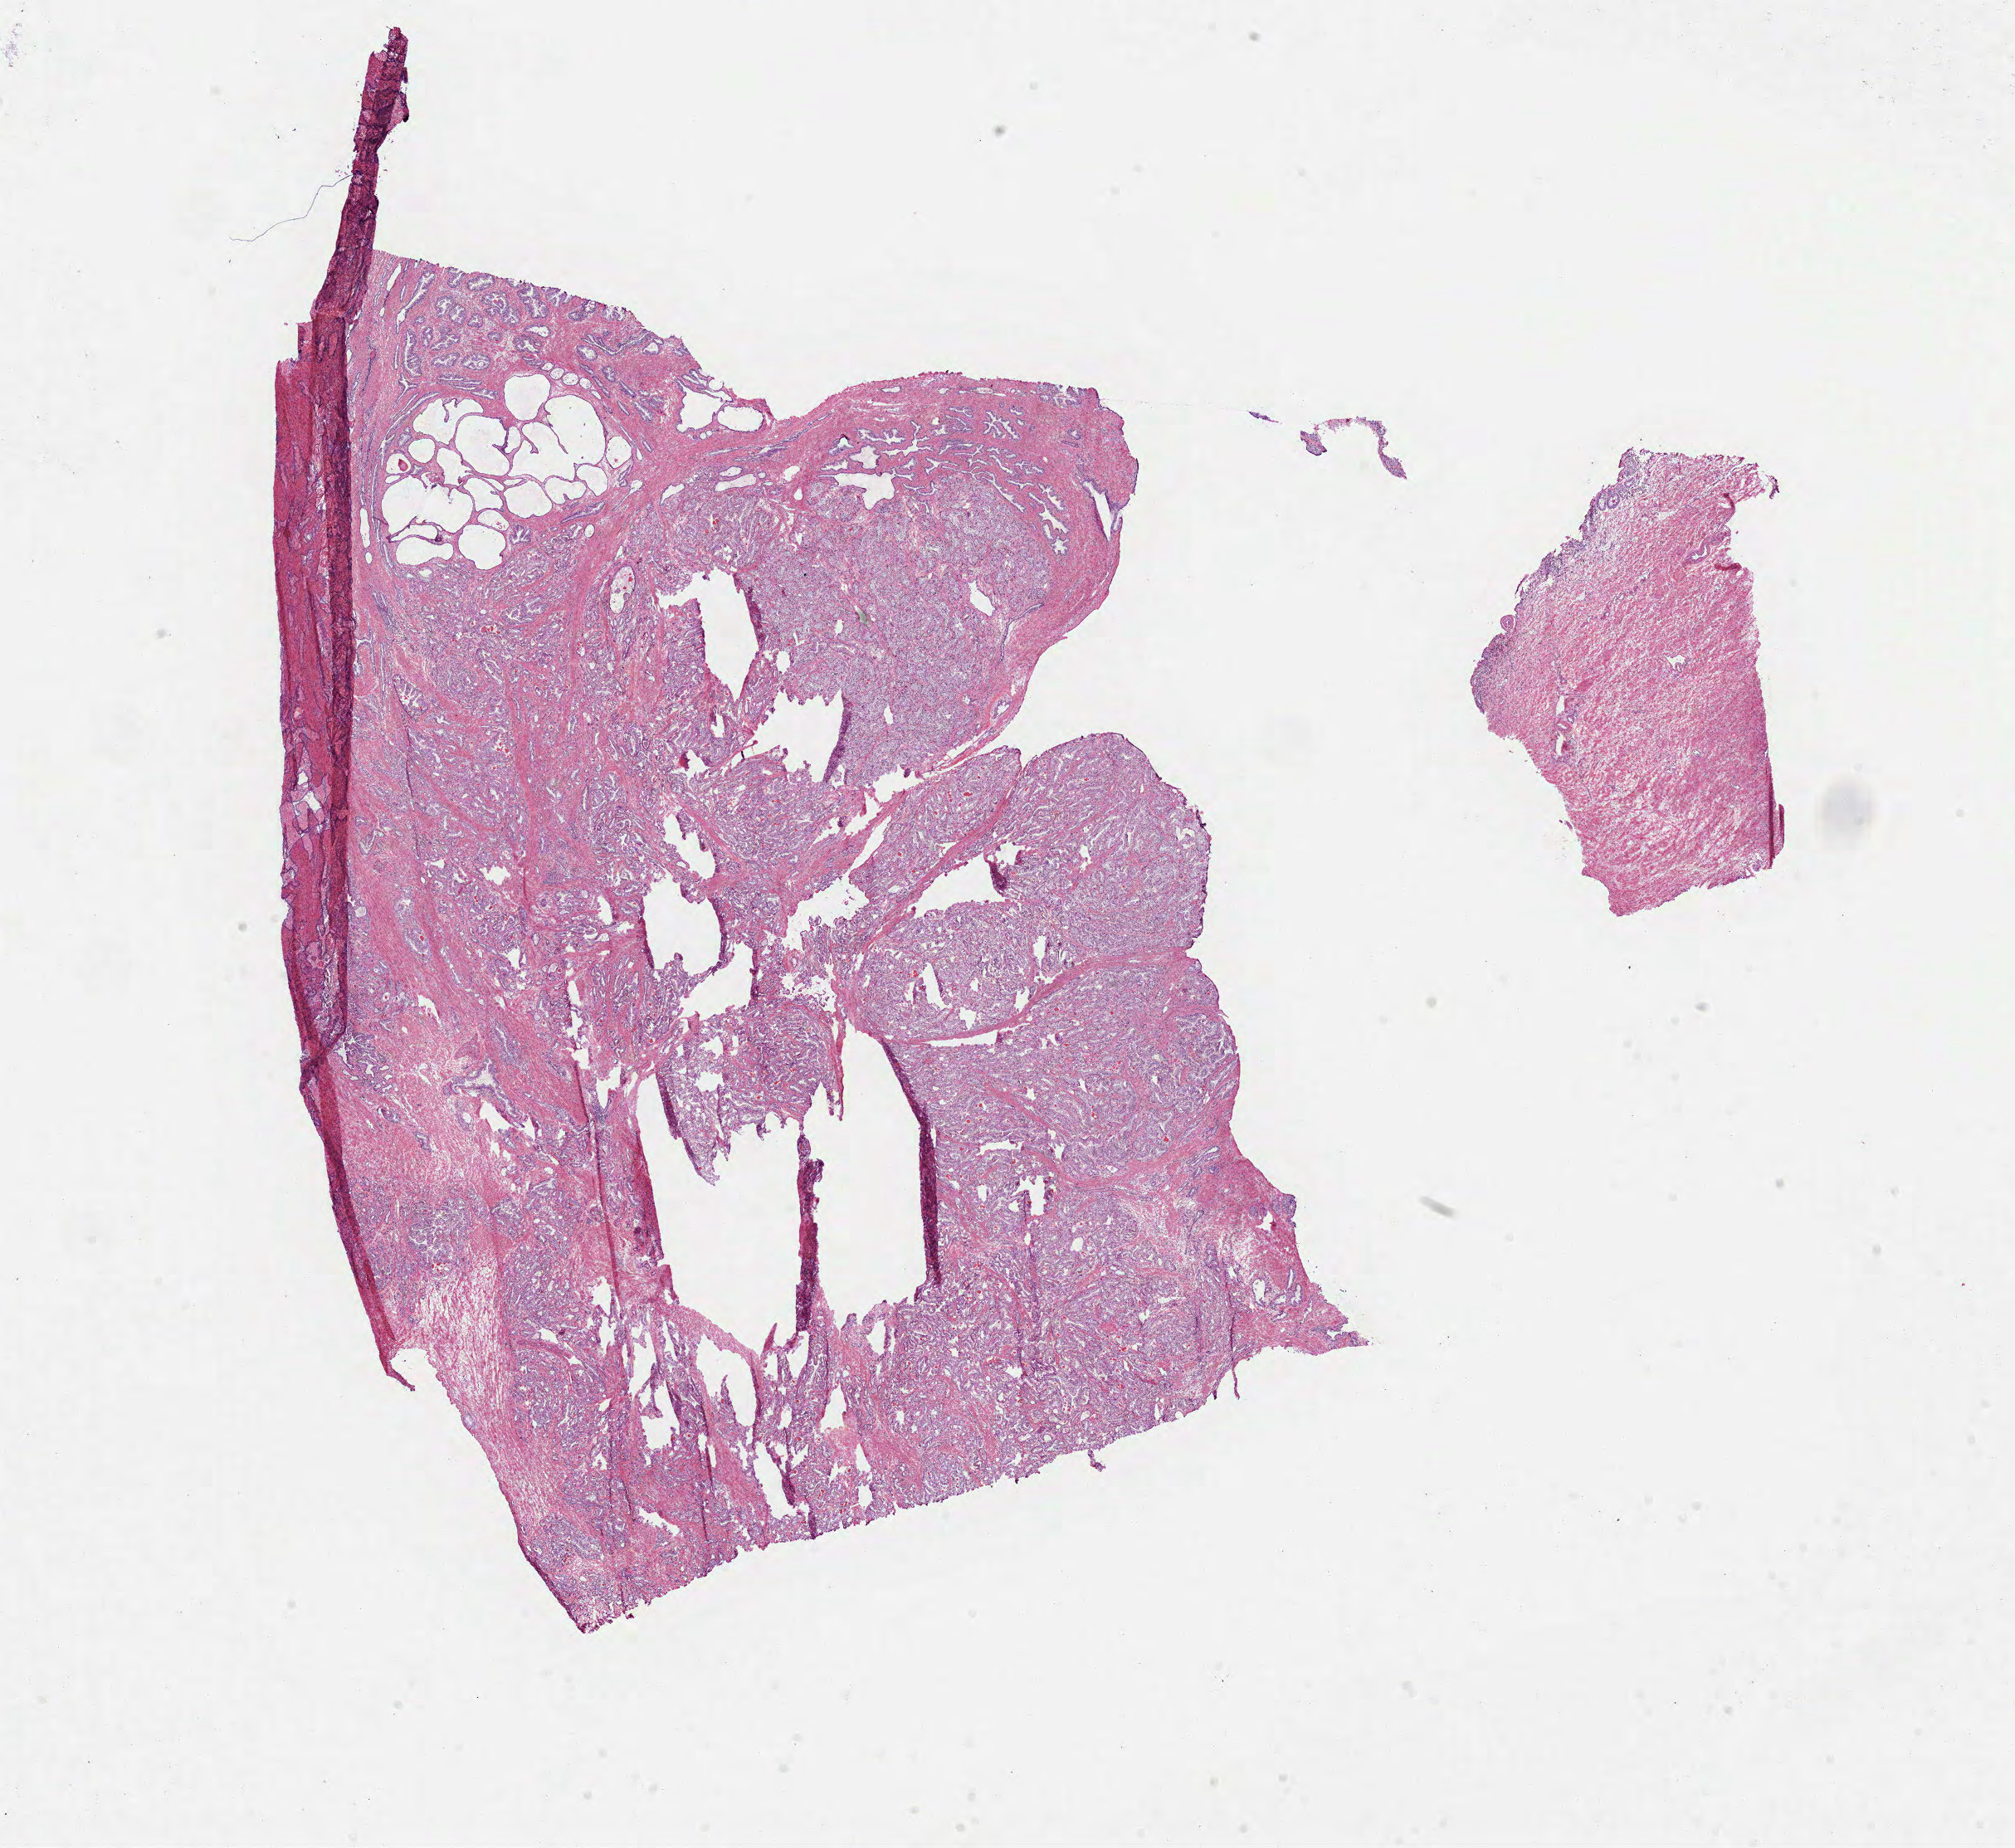
Whole-slide histology image, H&E-stained, low-resolution overview of the scanned area, about 19.6 x 18.0 mm (slide scanned at 40x); frozen section from the top of the tissue portion; sample: primary tumour, prostate. Male, age 67 years at initial diagnosis.
Pathologic diagnosis: Acinar cell carcinoma (prostate gland).